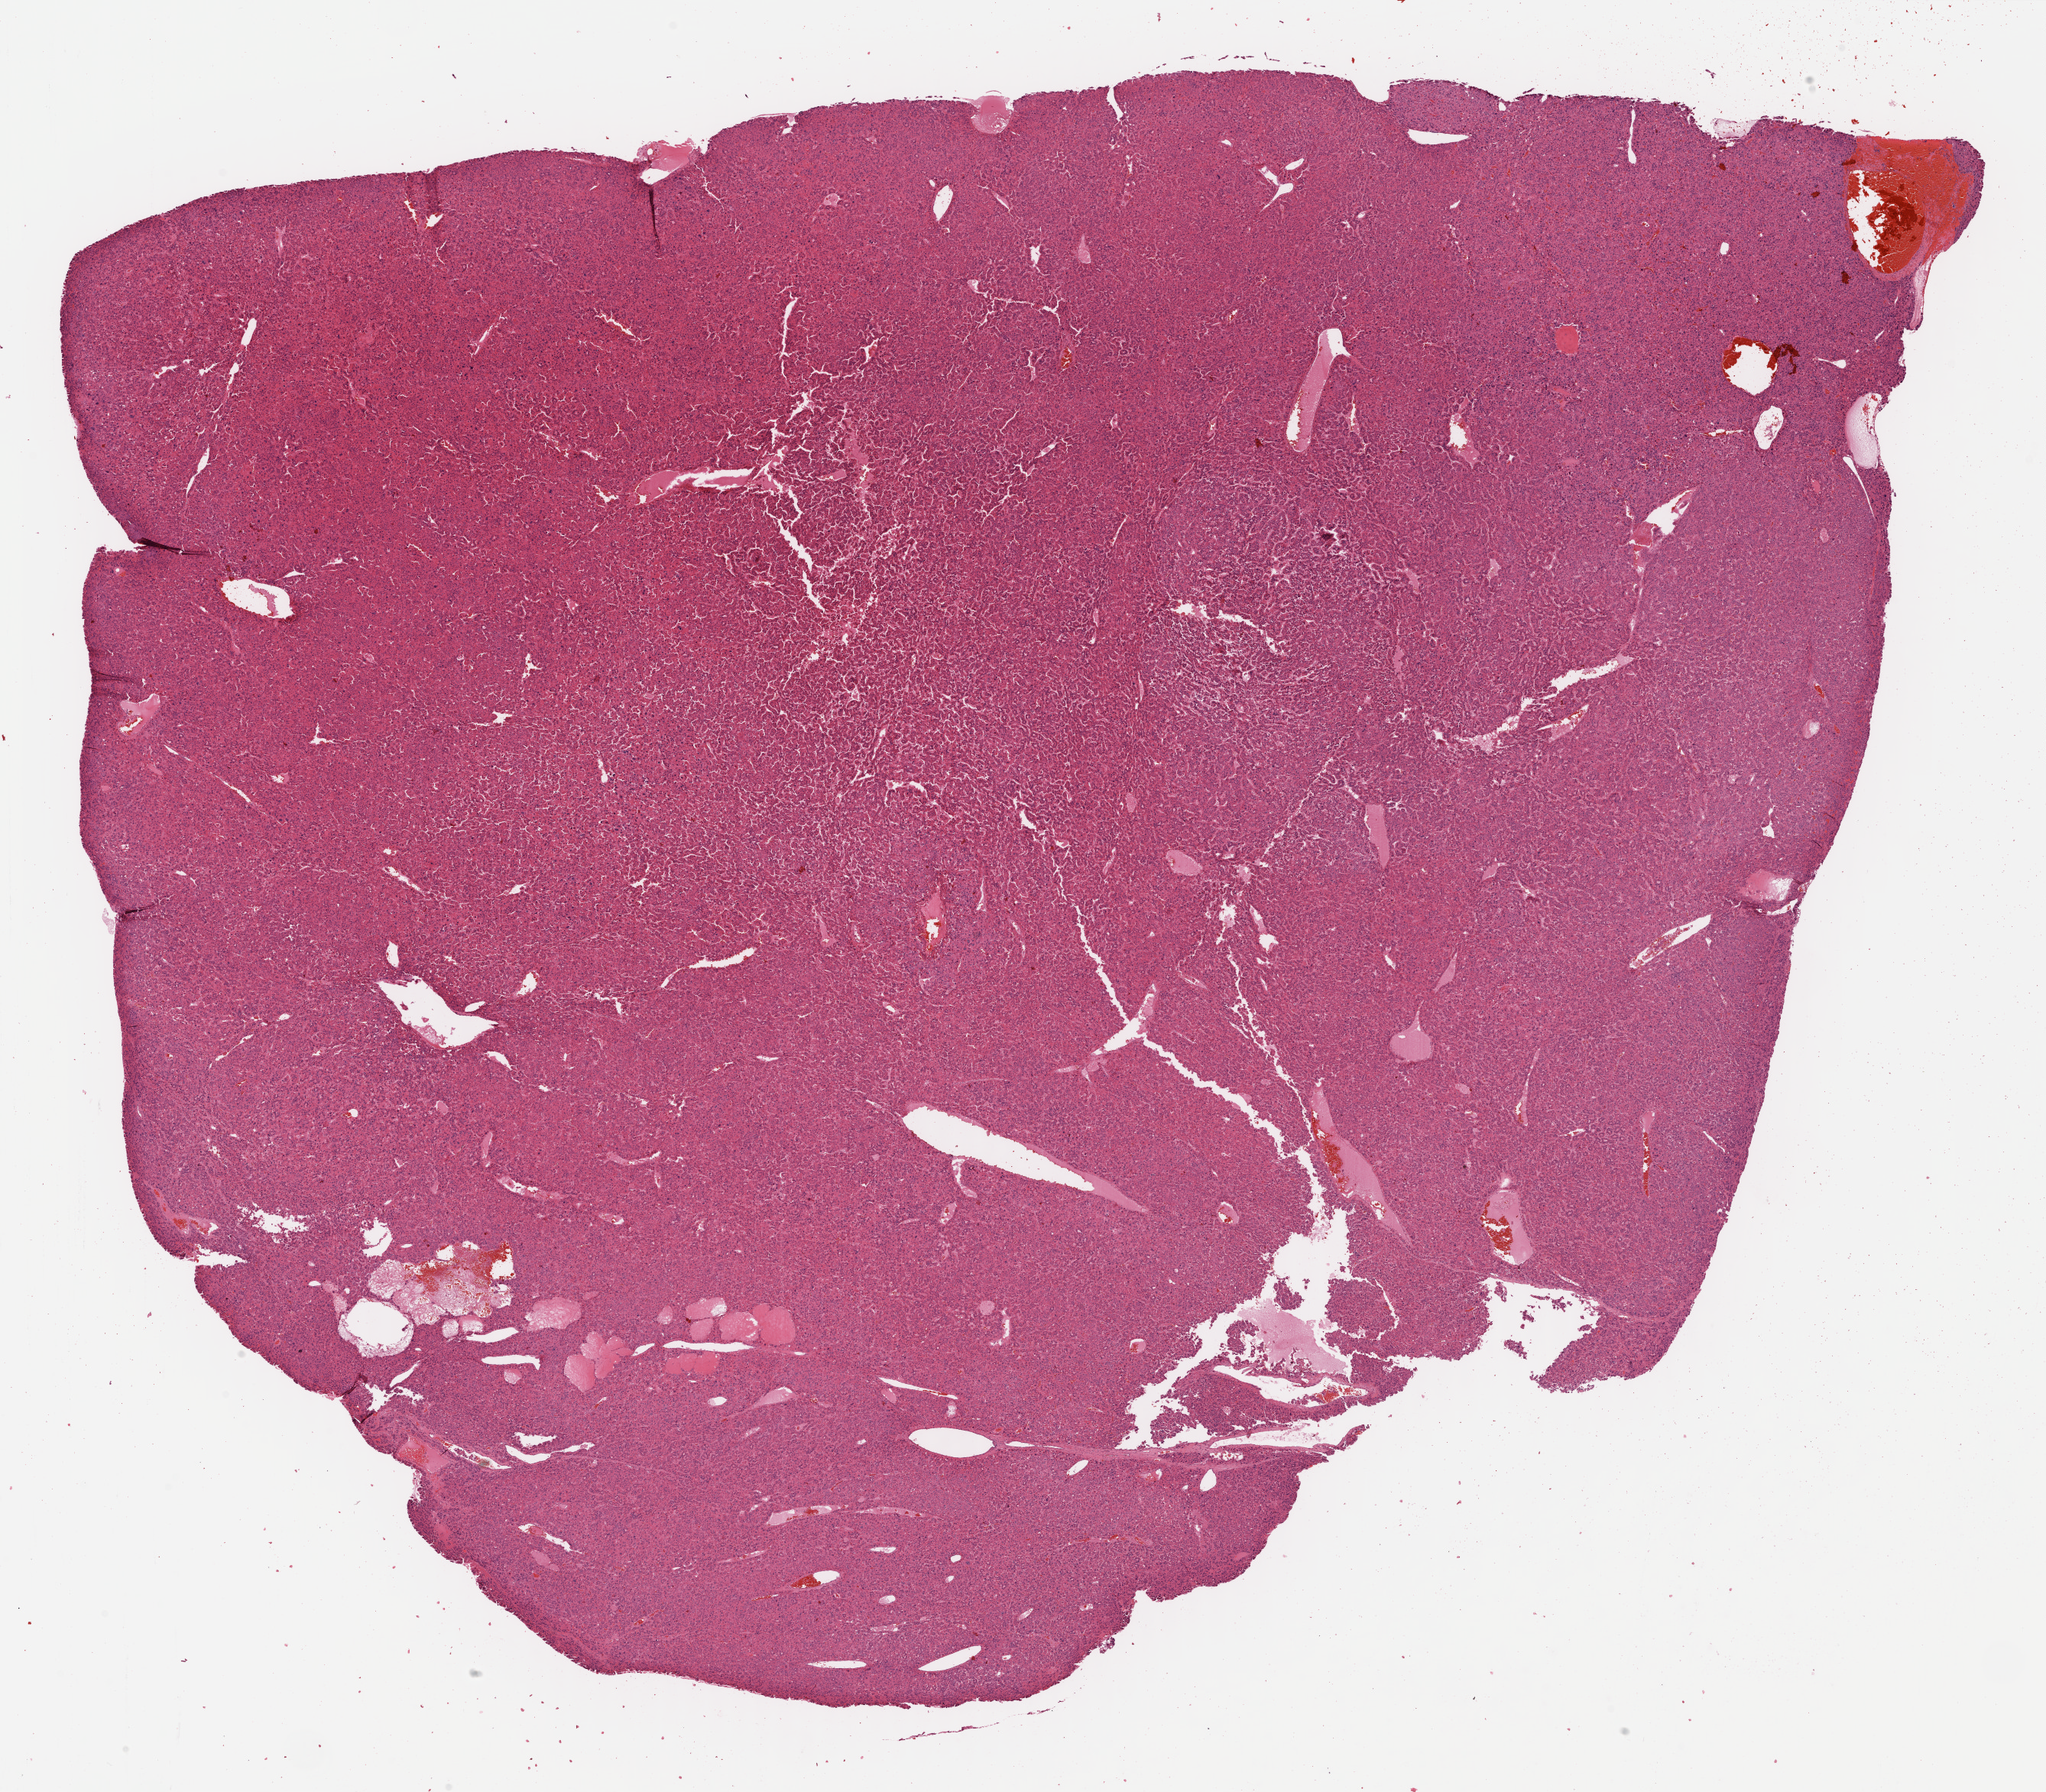
H&E whole-slide image — low-resolution overview of the scanned area, about 21.7 x 19.0 mm (slide scanned at 40x), formalin-fixed paraffin-embedded (FFPE) diagnostic section, primary tumour sample from the liver. Male patient; age at initial diagnosis 67 years. Histologic grade: G3 (poorly differentiated).
* AJCC pathologic stage: I (6th edition)
* diagnosis: Hepatocellular carcinoma, NOS